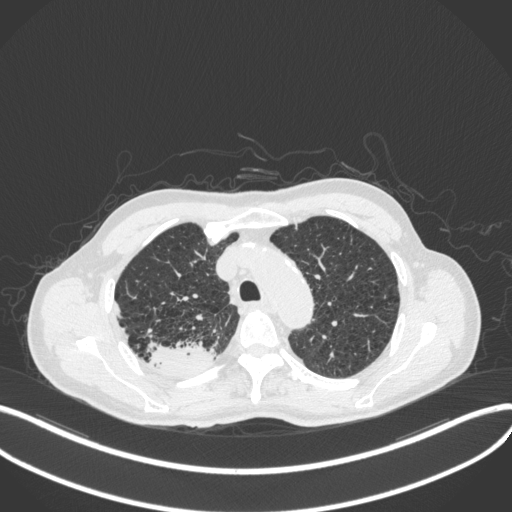
Chest CT, one axial slice. Position 339 of 423 along the scan axis. Reconstruction kernel B31f. 120 kVp. Lung window (W 1500 / L -600 HU). 512 × 512 image matrix, field of view 400 × 400 mm. Male patient, age 79 years. From the clinical record (not read from this slice): clinical TNM (as recorded): T3 N0 M0.
Annotated regions visible in this slice (bounding box drawn by a radiologist):
- lung tumour (recorded histology: adenocarcinoma): bounding box (x1, y1, x2, y2) in pixels: (143, 337, 214, 381)